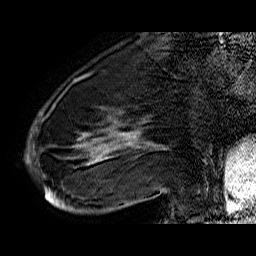
Breast MRI (dynamic contrast-enhanced), one sagittal slice. Position 17 of 60 along the scan axis. Dynamic contrast-enhanced series, time point 2 of 6 at this slice position (early post-contrast). 1.5 T. TE 6.4 ms, TR 32.9 ms. 4 mm slice thickness. 256 × 256 image matrix, field of view 200 × 200 mm. Female patient. Case-level facts recorded for this patient, not image findings: setting: breast cancer imaged before/during neoadjuvant chemotherapy; receptor status: HR-positive, HER2-negative.
Structures marked on this image (semi-automatically segmented with operator editing):
- analysis volume of interest (the breast-tissue region the enhancement analysis was run in; not a lesion): bounding box <41,74,176,210> (left, top, right, bottom; pixels)
- tumour enhancement mask (voxels above the 100 % enhancement threshold inside the analysis volume of interest): <44,125,165,207>